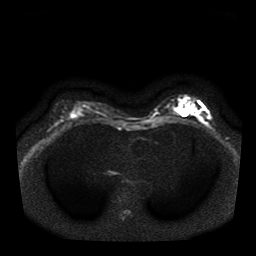
Breast MRI, one axial slice; position 20 of 41 along the scan axis; diffusion-weighted series; image 2 of 4 stored at this slice position (different b-values; order by instance number); 1.5 T; 5 mm slice thickness; 256 × 256 image matrix, field of view 330 × 330 mm. Female patient.
Annotated regions visible in this slice (manually delineated by an expert):
- tumour on diffusion-weighted imaging: bounding box (x1, y1, x2, y2) in pixels: (190, 107, 198, 116)